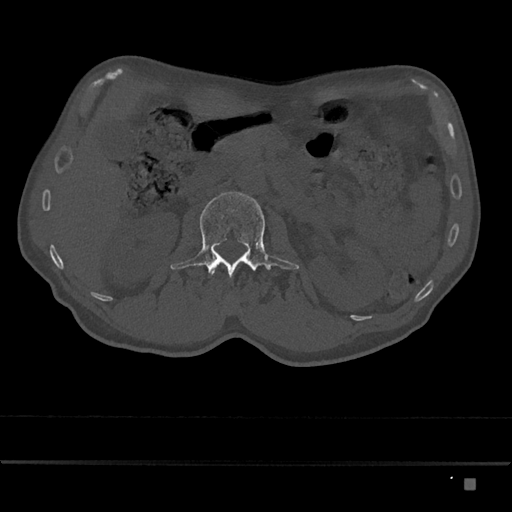
CT including the spine, one axial slice; slice 484 of 797 in the series (ordered by position); 120 kVp; bone window (W 1800 / L 400 HU); 0.5 mm slice thickness; 512 × 512 image matrix. Male patient, age 72 years. From the clinical record (not read from this slice): primary cancer: prostate.
Structures marked on this image (semi-automatic segmentation, software-assisted and operator-edited):
- L1 vertebra: bounding box (x1, y1, x2, y2) in pixels: (210, 271, 215, 275)
- L2 vertebra: (170, 191, 299, 278)